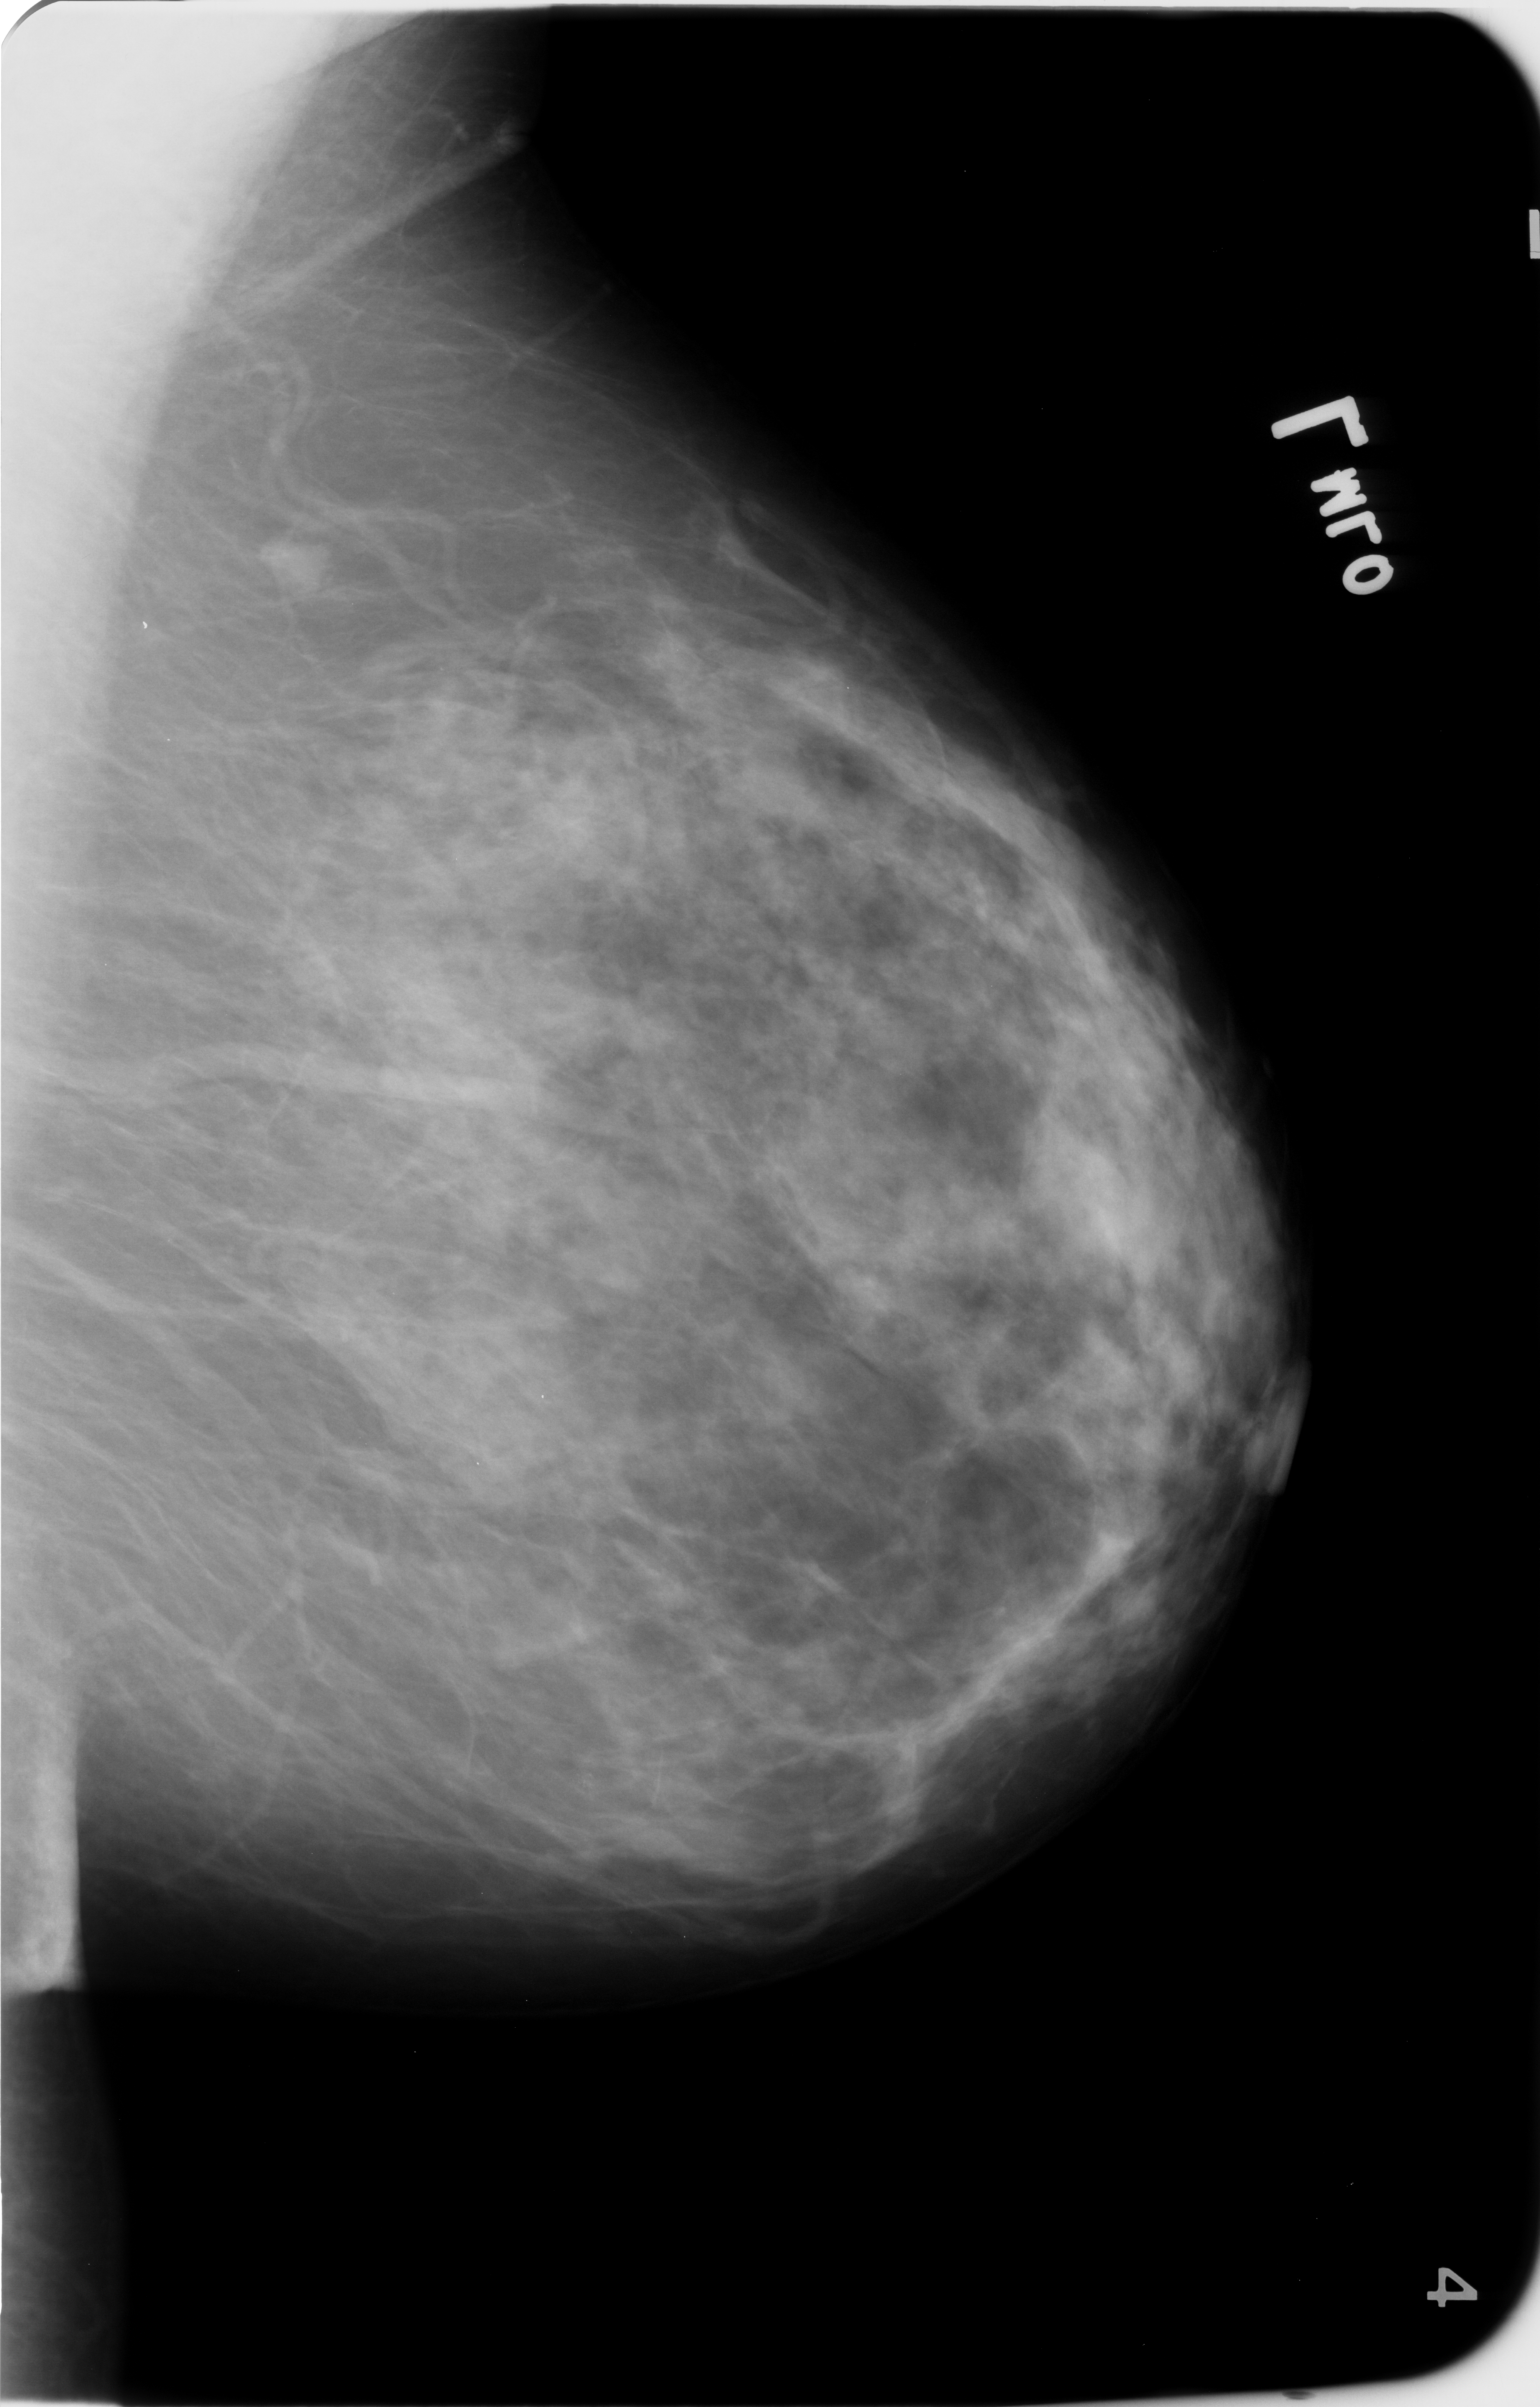
Digitized screen-film mammogram, left breast, MLO view.
Radiologist-marked abnormalities on this image: calcifications, morphology pleomorphic, distribution clustered; BI-RADS assessment category 4; subtlety rating 3 on a 1 (subtle) to 5 (obvious) scale; pathology (as recorded): benign.